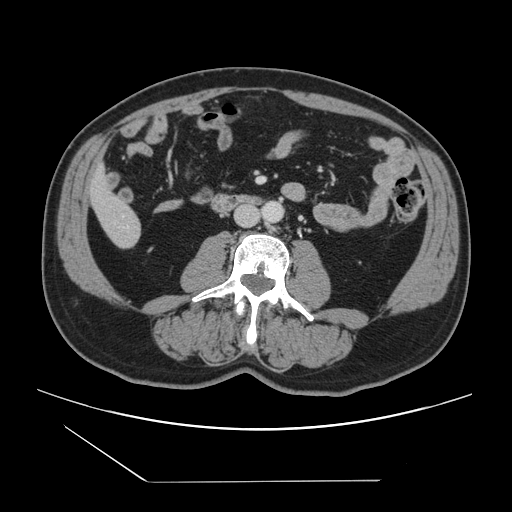
Contrast-enhanced abdominal CT, one axial slice; slice 20 of 157 in the series (ordered by position); 120 kVp; intravenous contrast given; soft-tissue window (W 400 / L 40 HU); 2.5 mm slice thickness; 512 × 512 image matrix, field of view 407 × 407 mm. Male patient, age 61 years. Case-level facts recorded for this patient, not image findings: diagnosis: colorectal cancer liver metastases, imaged before liver resection; multiple liver metastases: yes; largest metastasis: 5.5 cm.
Structures marked on this image (manually delineated by an expert):
- liver: bounding box <91,170,141,247> (left, top, right, bottom; pixels)
- planned liver remnant (the part of the liver to remain after resection): <91,170,128,218>